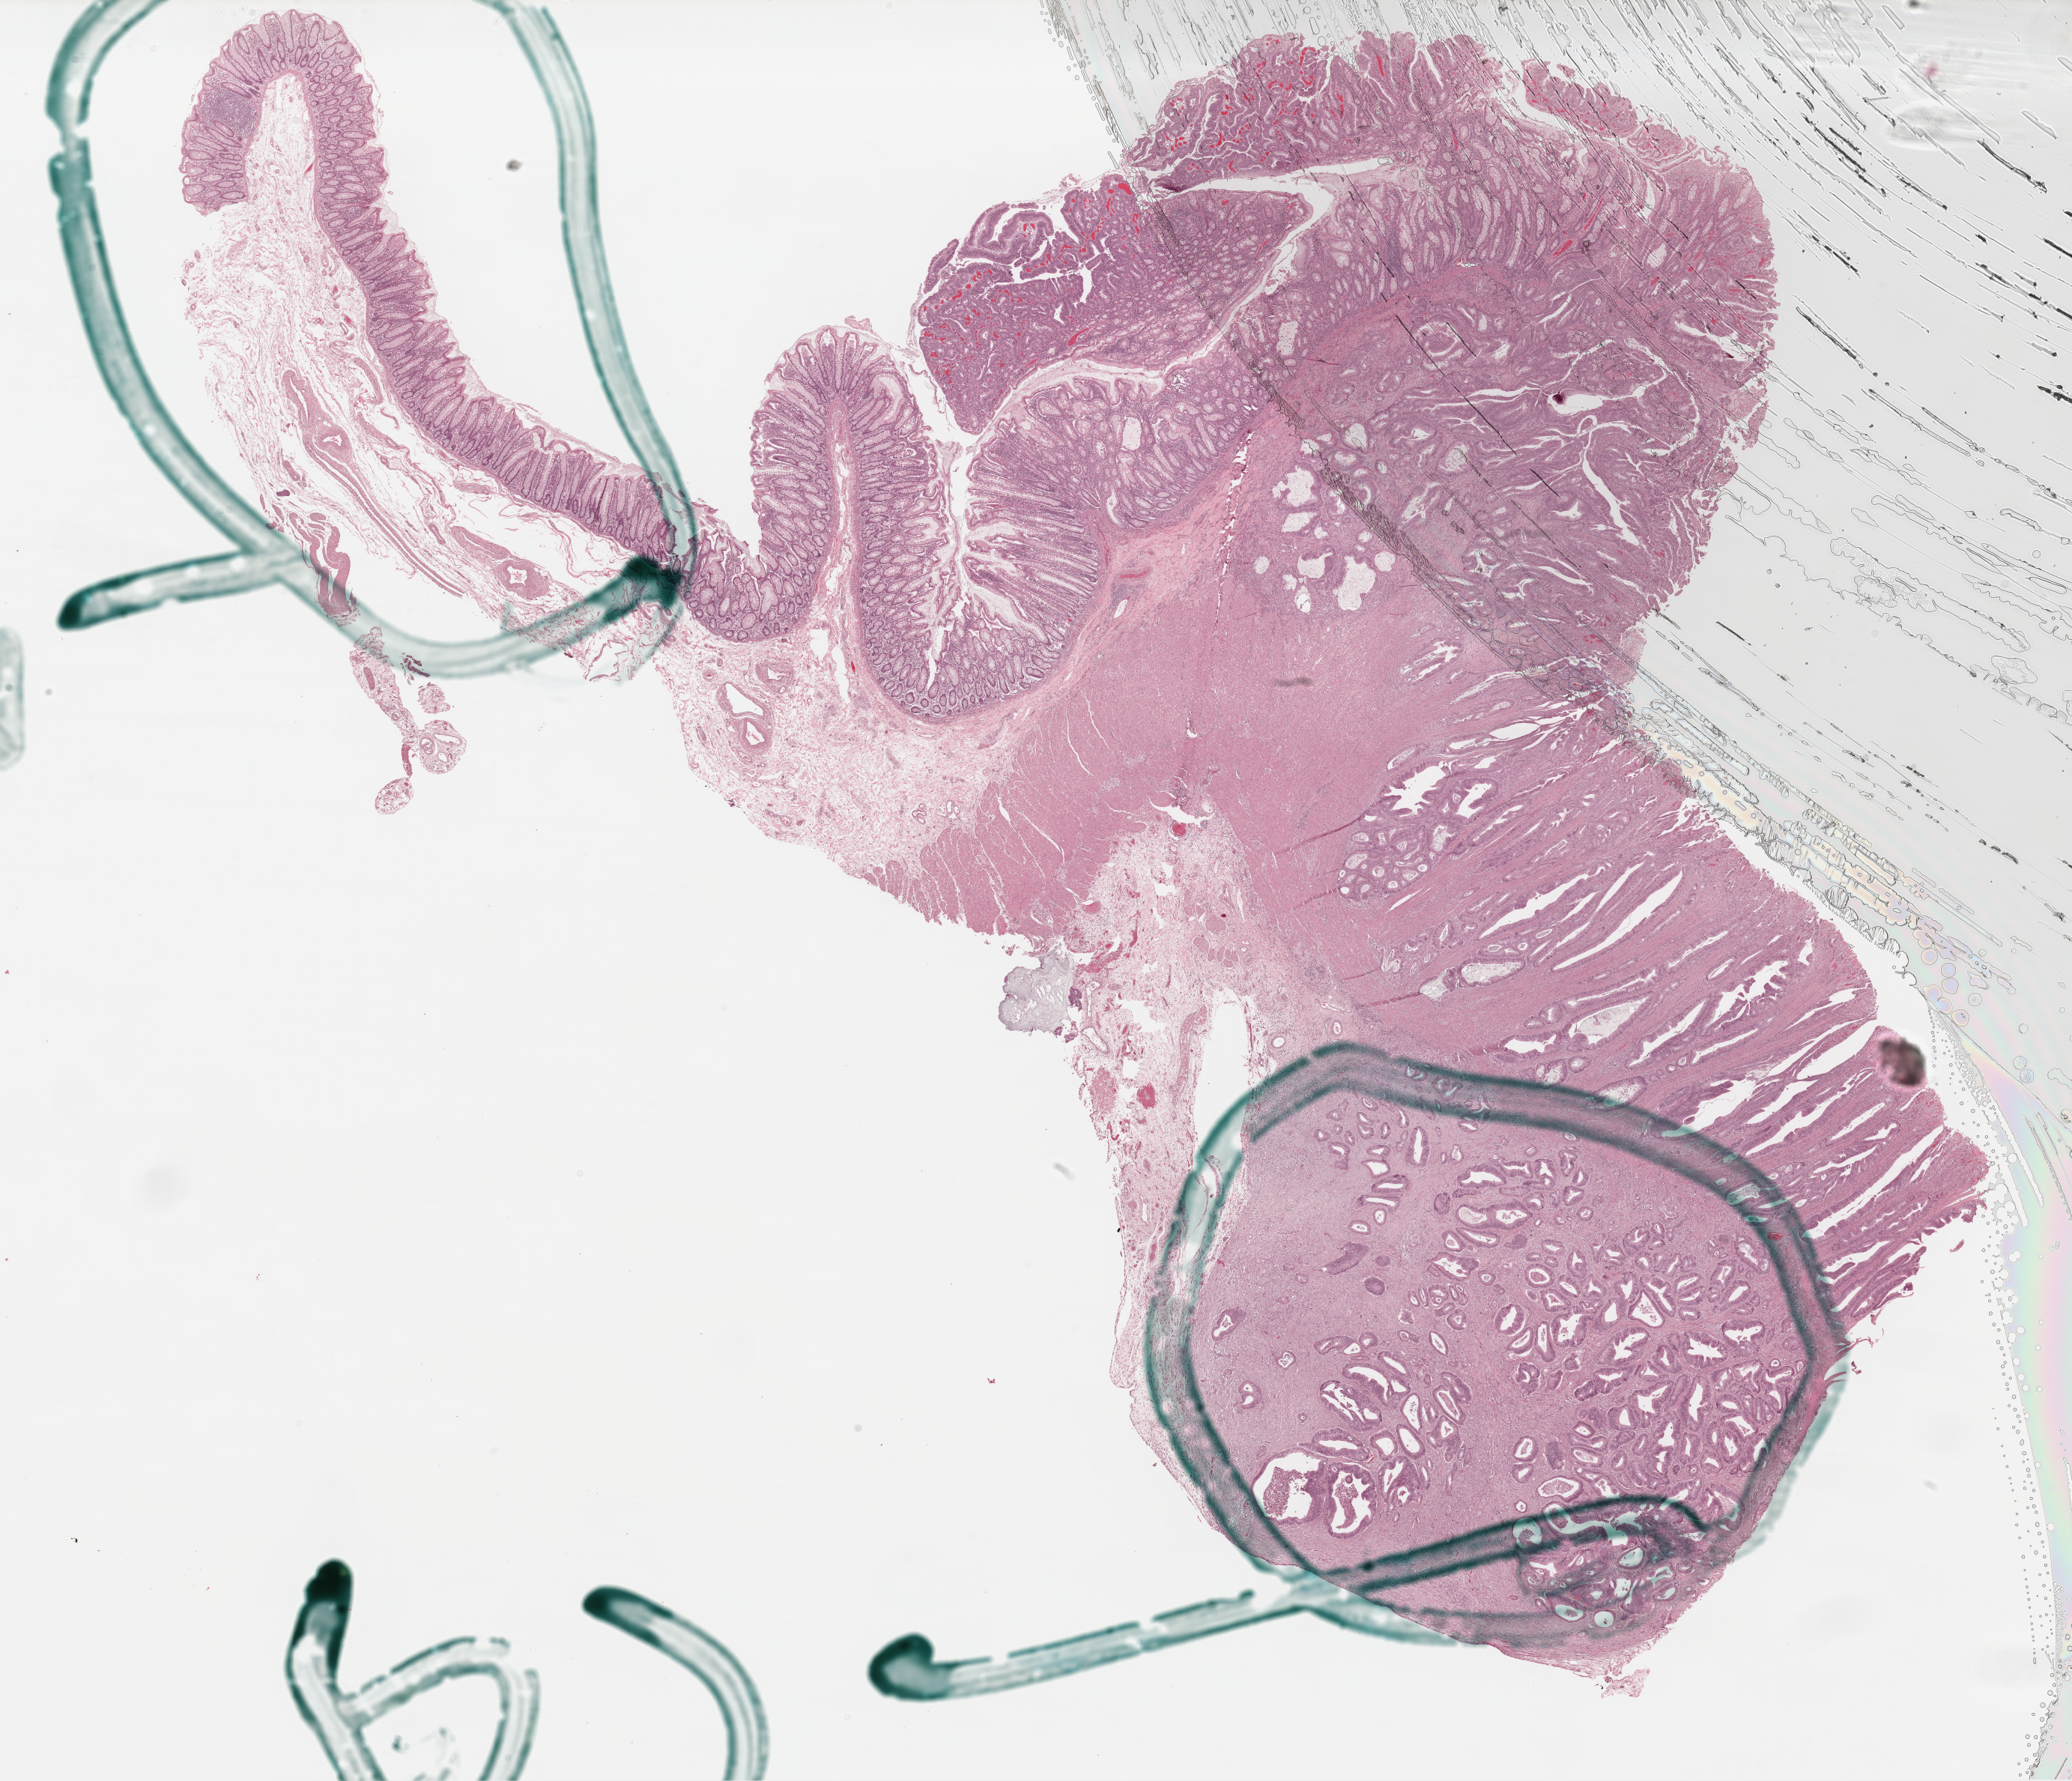
H&E-stained whole-slide image, shown as a low-resolution overview of the whole scanned area (about 21.9 x 18.8 mm); FFPE section; colon, primary tumour sample. Male patient; age at initial diagnosis 80 years.
Histologic diagnosis: Adenocarcinoma, NOS (cecum).